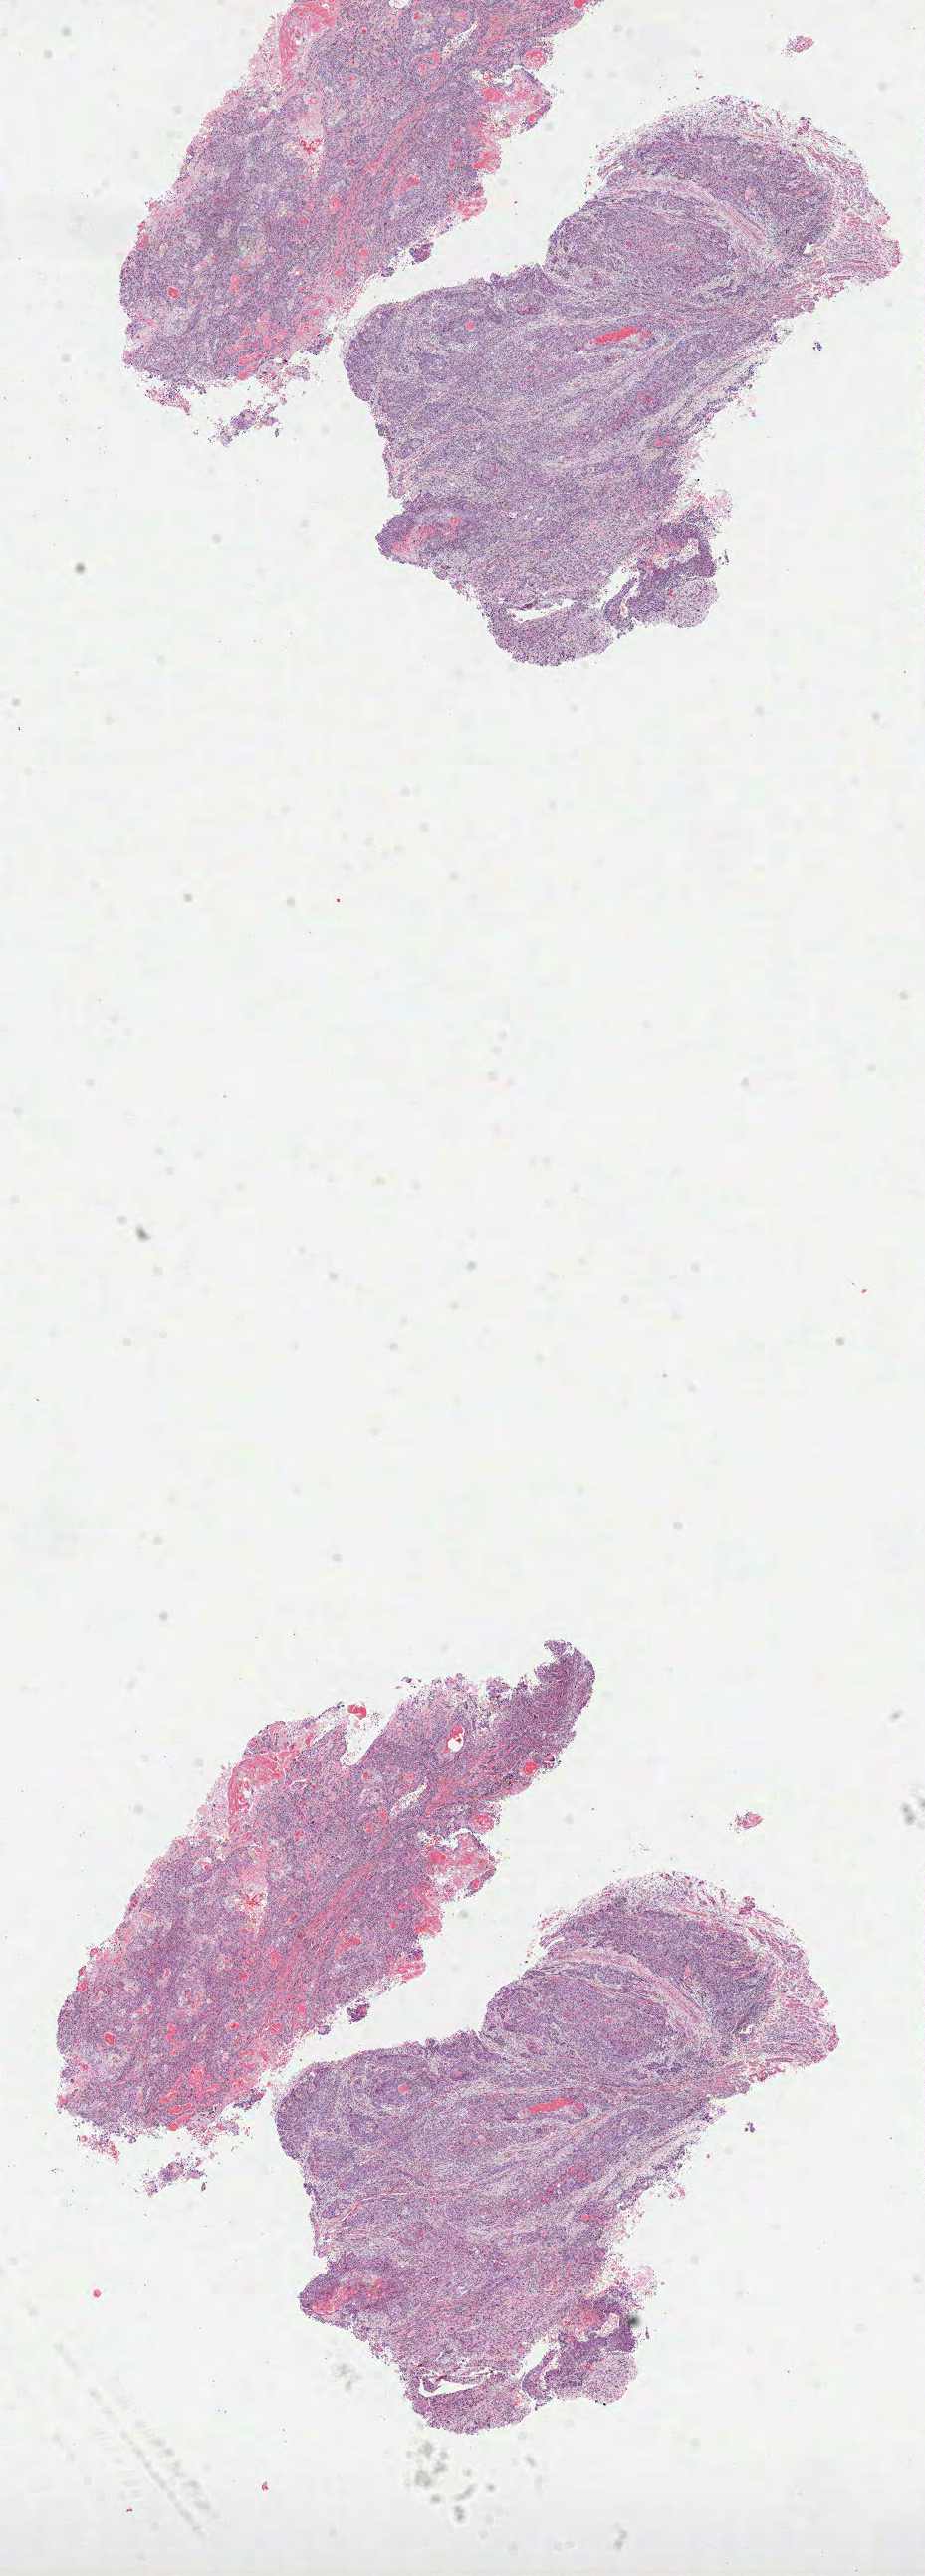
Hematoxylin and eosin (H&E) stained whole-slide image, shown as a low-resolution overview of the whole scanned area (about 7.5 x 20.9 mm, slide scanned at 40x); formalin-fixed paraffin-embedded (FFPE) diagnostic section; primary tumour sample from the head and neck. Male patient; age at initial diagnosis 49 years. Histologic grade: G3 (poorly differentiated).
• diagnosis: Squamous cell carcinoma, NOS (larynx, NOS)
• AJCC pathologic stage: IVA